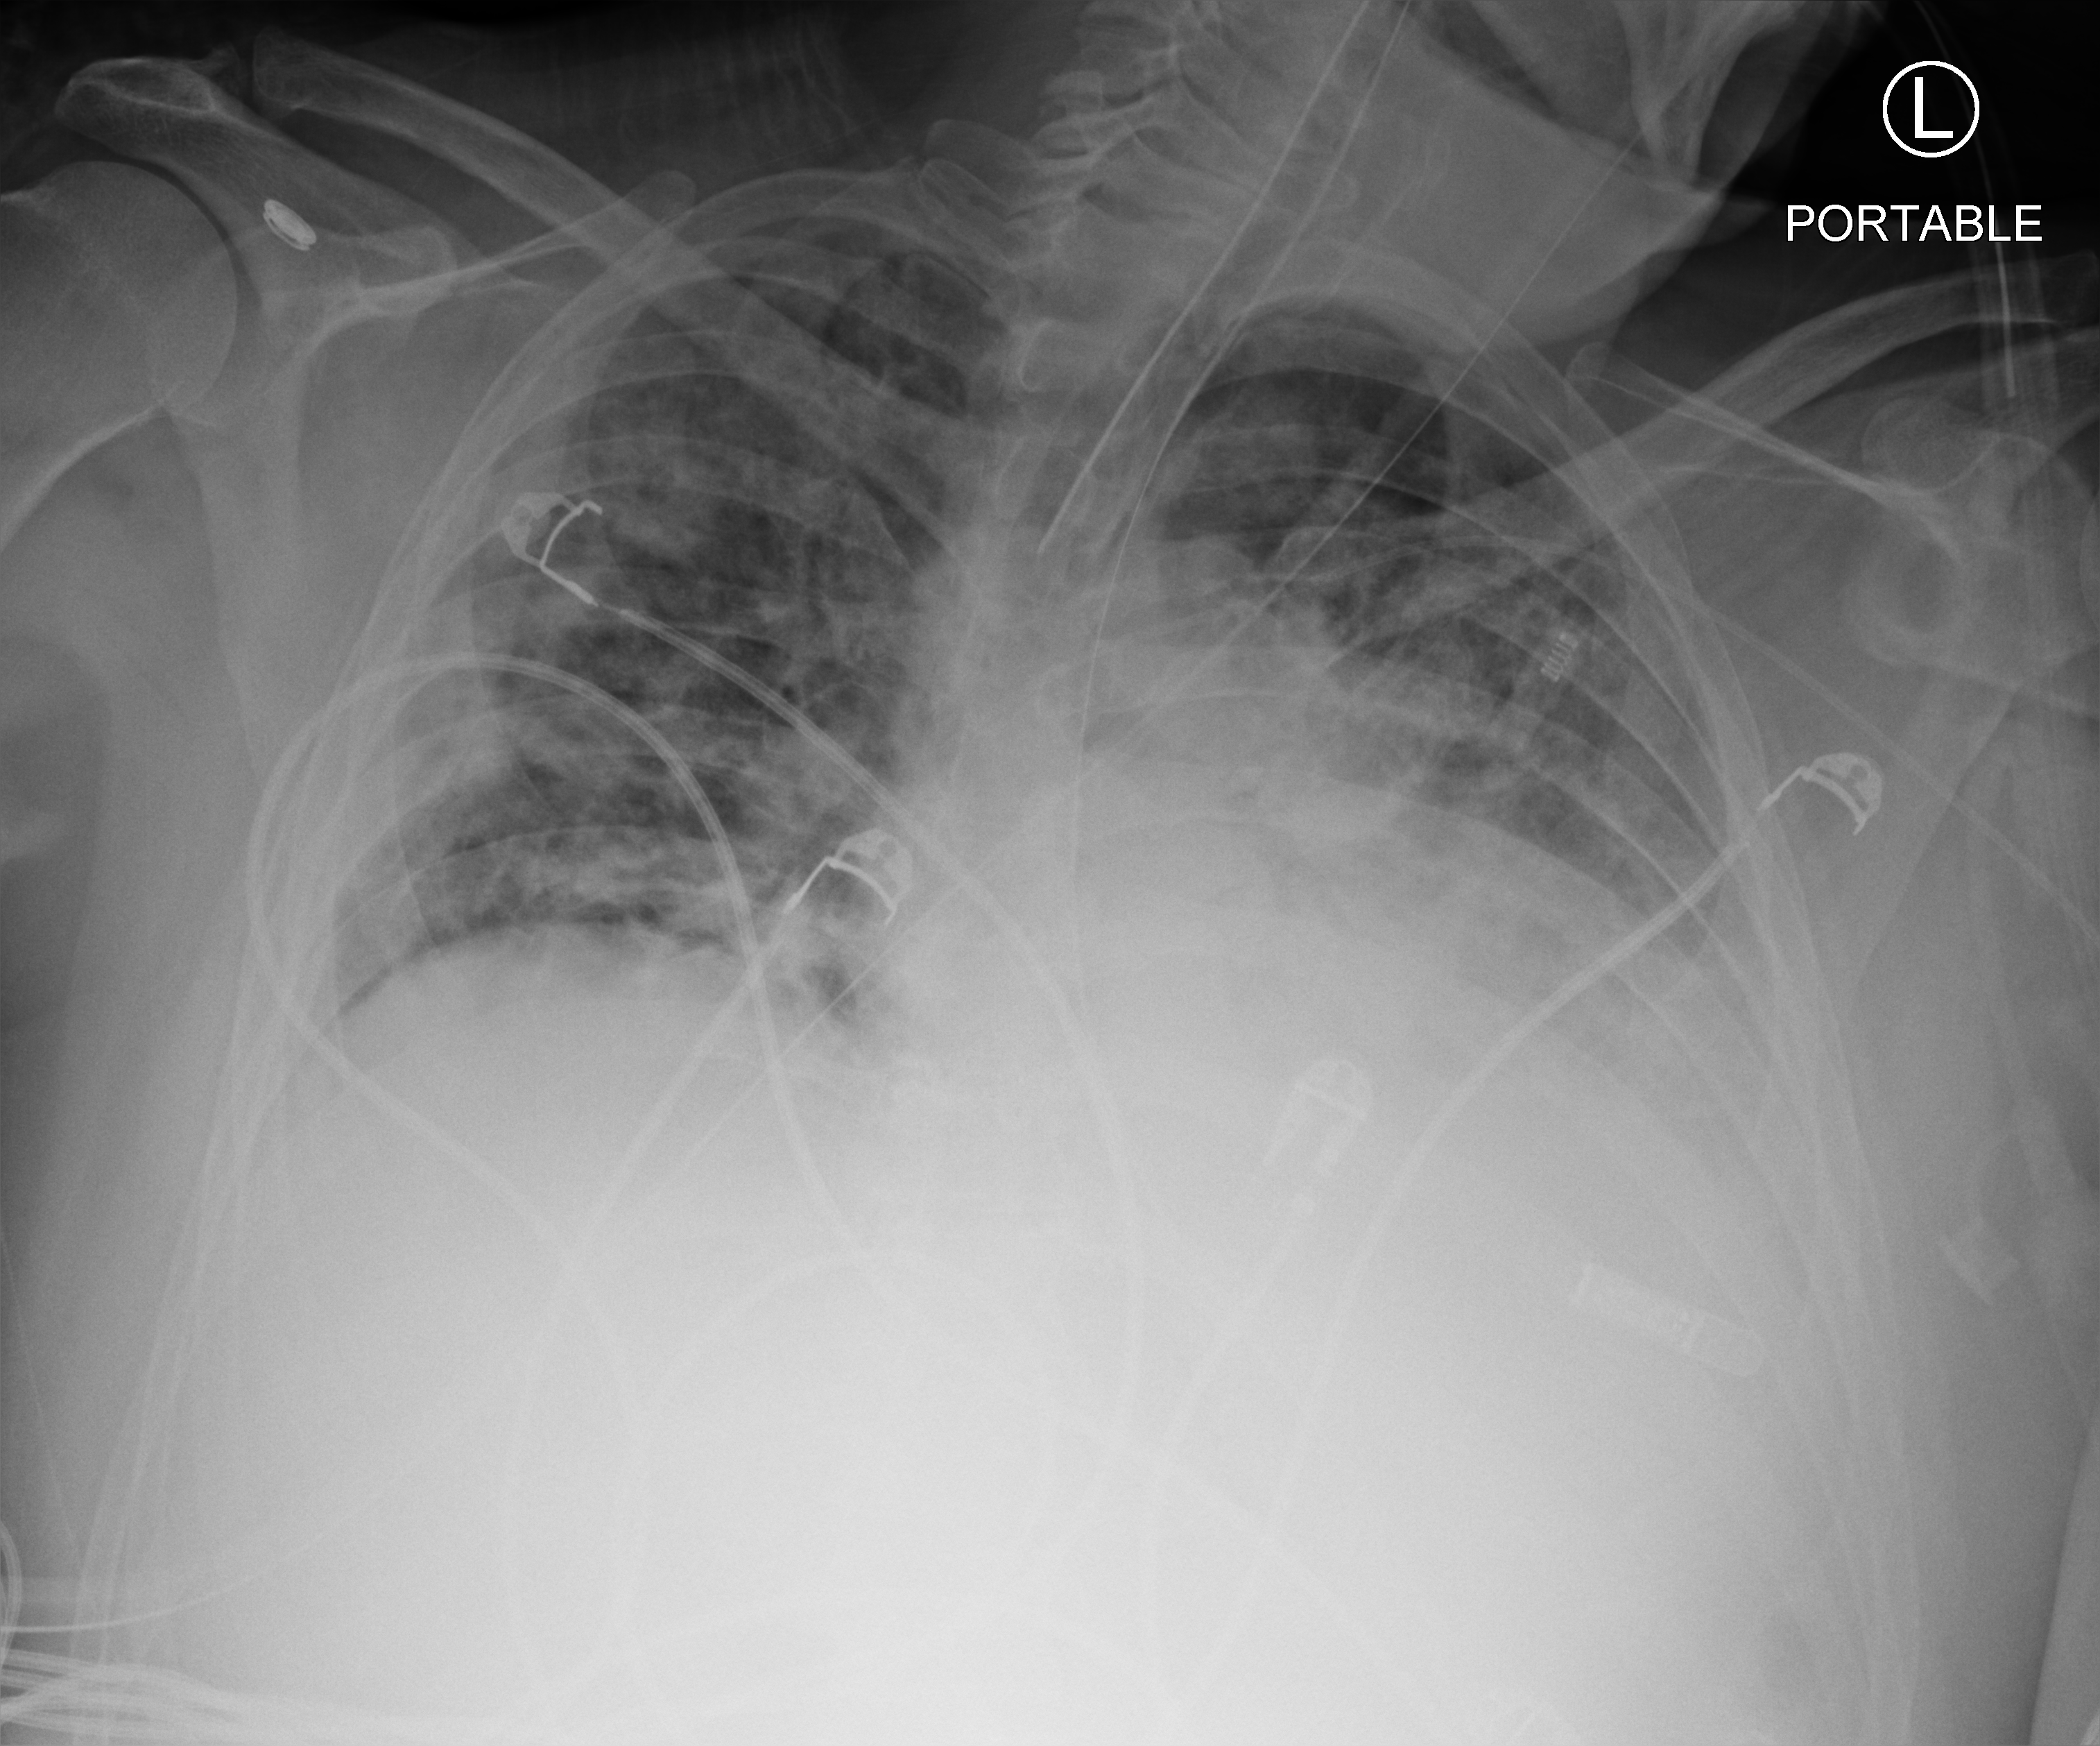
Portable chest radiograph, anteroposterior (AP) projection. Patient hospitalised with COVID-19; male, aged 18–59 years.
Hospital-stay facts (about this admission, not read from this image; timing relative to this image not recorded): chronic kidney disease (admission record): no.